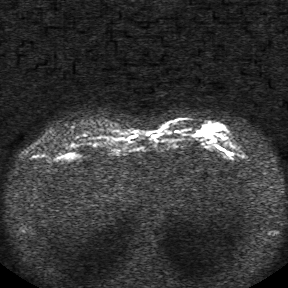
Breast MRI, one axial slice. Slice 7 of 34 in the series (ordered by position). Diffusion-weighted series; image 2 of 4 stored at this slice position (different b-values; order by instance number). 1.5 T. 5 mm slice thickness. 288 × 288 image matrix, field of view 340 × 340 mm. Female patient.
Annotated regions visible in this slice (outlined manually by an expert reader):
- tumour on diffusion-weighted imaging: box from (x=205, y=127) to (x=219, y=134) px